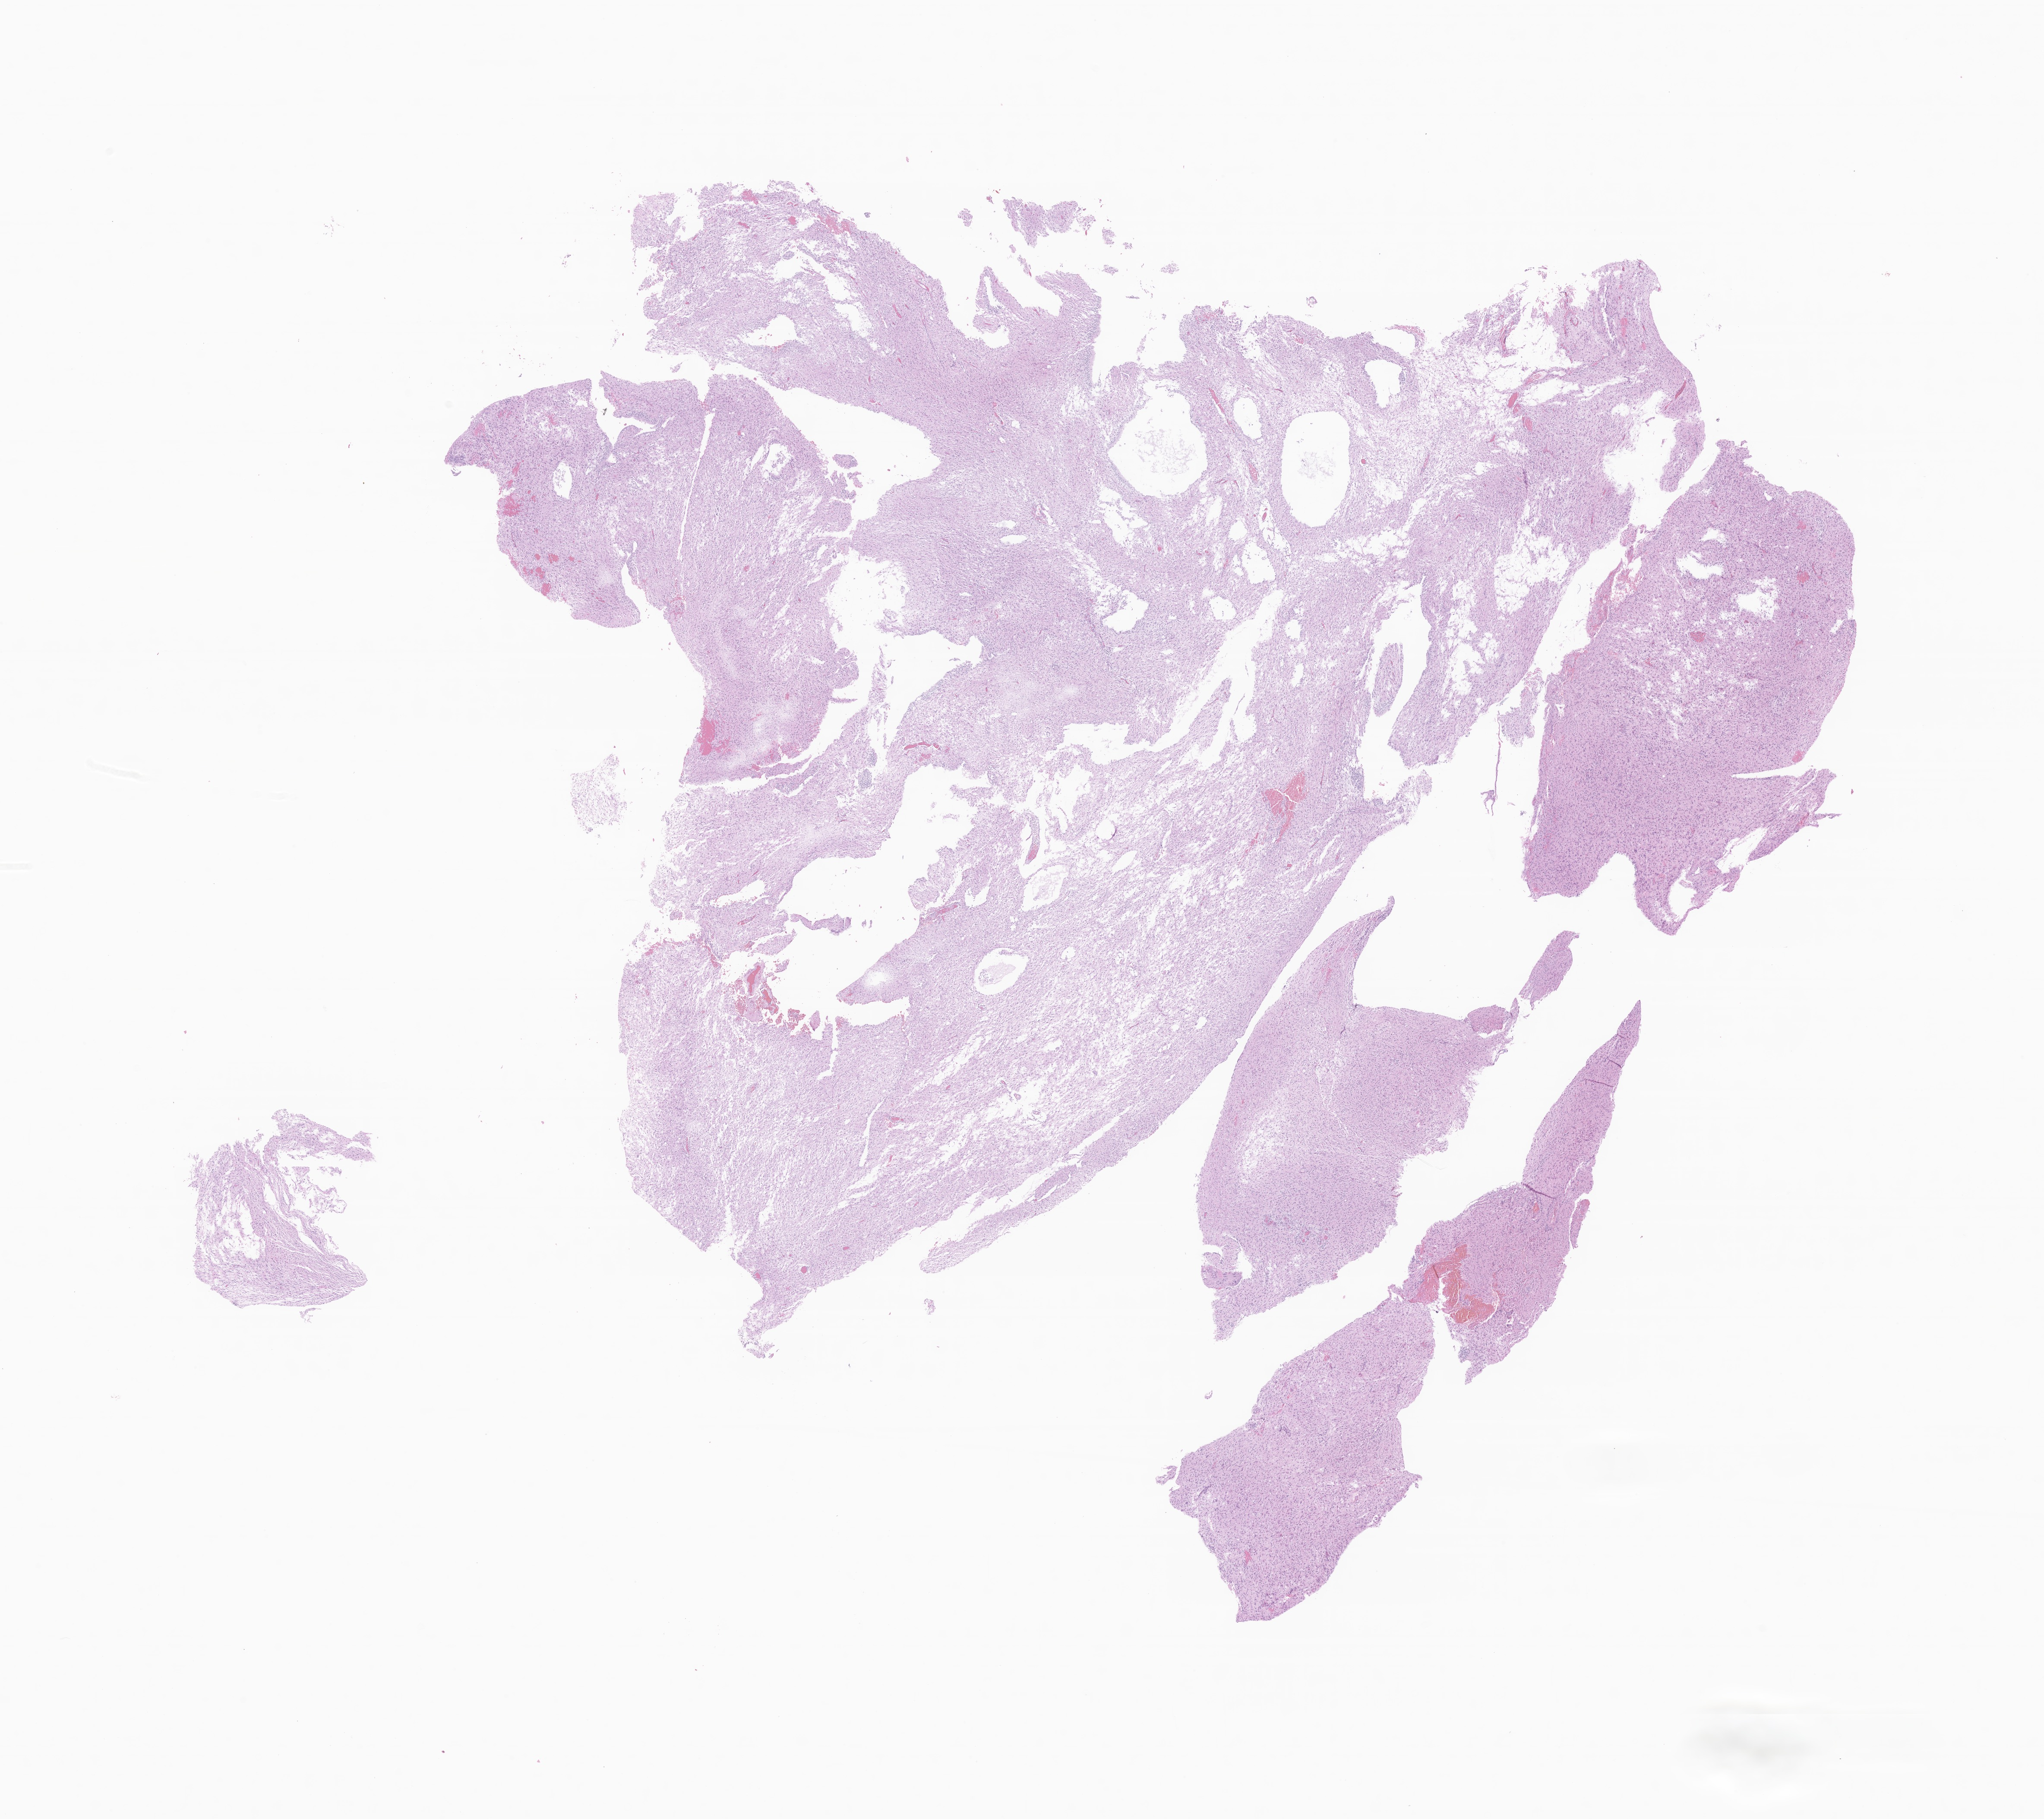
Whole-slide image, hematoxylin and eosin (H&E) stain of tumor tissue from the brain, whole scanned area (about 20.0 x 17.8 mm) shown as a low-resolution overview, formalin-fixed paraffin-embedded section. Patient: male, age 156 months (13 years).
Diagnosis (ICD-O-3 morphology term): Ganglioglioma, NOS.